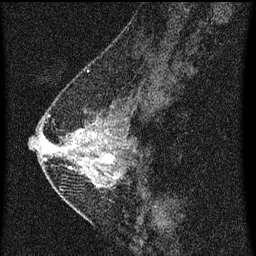
Breast MRI (dynamic contrast-enhanced), one sagittal slice. Position 24 of 60 along the scan axis. Dynamic contrast-enhanced series, image 2 of 3 at this slice position (ordered by acquisition). 1.5 T. TE 4.2 ms, TR 8 ms. 2 mm slice thickness. 256 × 256 image matrix. Patient: female, 47 years.
Structures marked on this image (semi-automatic segmentation, software-assisted and operator-edited):
- analysis volume of interest (the breast-tissue region the enhancement analysis was run in; not a lesion): bounding box (x1, y1, x2, y2) in pixels: (42, 92, 140, 199)
- tumour enhancement mask (voxels above the 70 % enhancement threshold inside the analysis volume of interest): (45, 130, 115, 187)